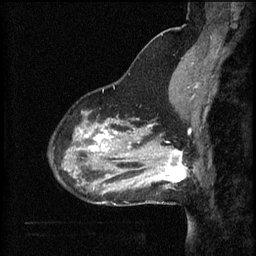
Breast MRI (dynamic contrast-enhanced), one sagittal slice; position 18 of 60 along the scan axis; 3 images stored at this slice position (order not interpretable as contrast timing); 1.5 T; TE 4.2 ms, TR 8.2 ms; 2 mm slice thickness; 256 × 256 image matrix, field of view 200 × 200 mm. Patient: female, 37 years.
Annotated regions visible in this slice (semi-automatically segmented with operator editing):
- analysis volume of interest (the breast-tissue region the enhancement analysis was run in; not a lesion): bounding box (x1, y1, x2, y2) in pixels: (148, 140, 191, 187)
- tumour enhancement mask (voxels above the 70 % enhancement threshold inside the analysis volume of interest): (152, 150, 187, 183)